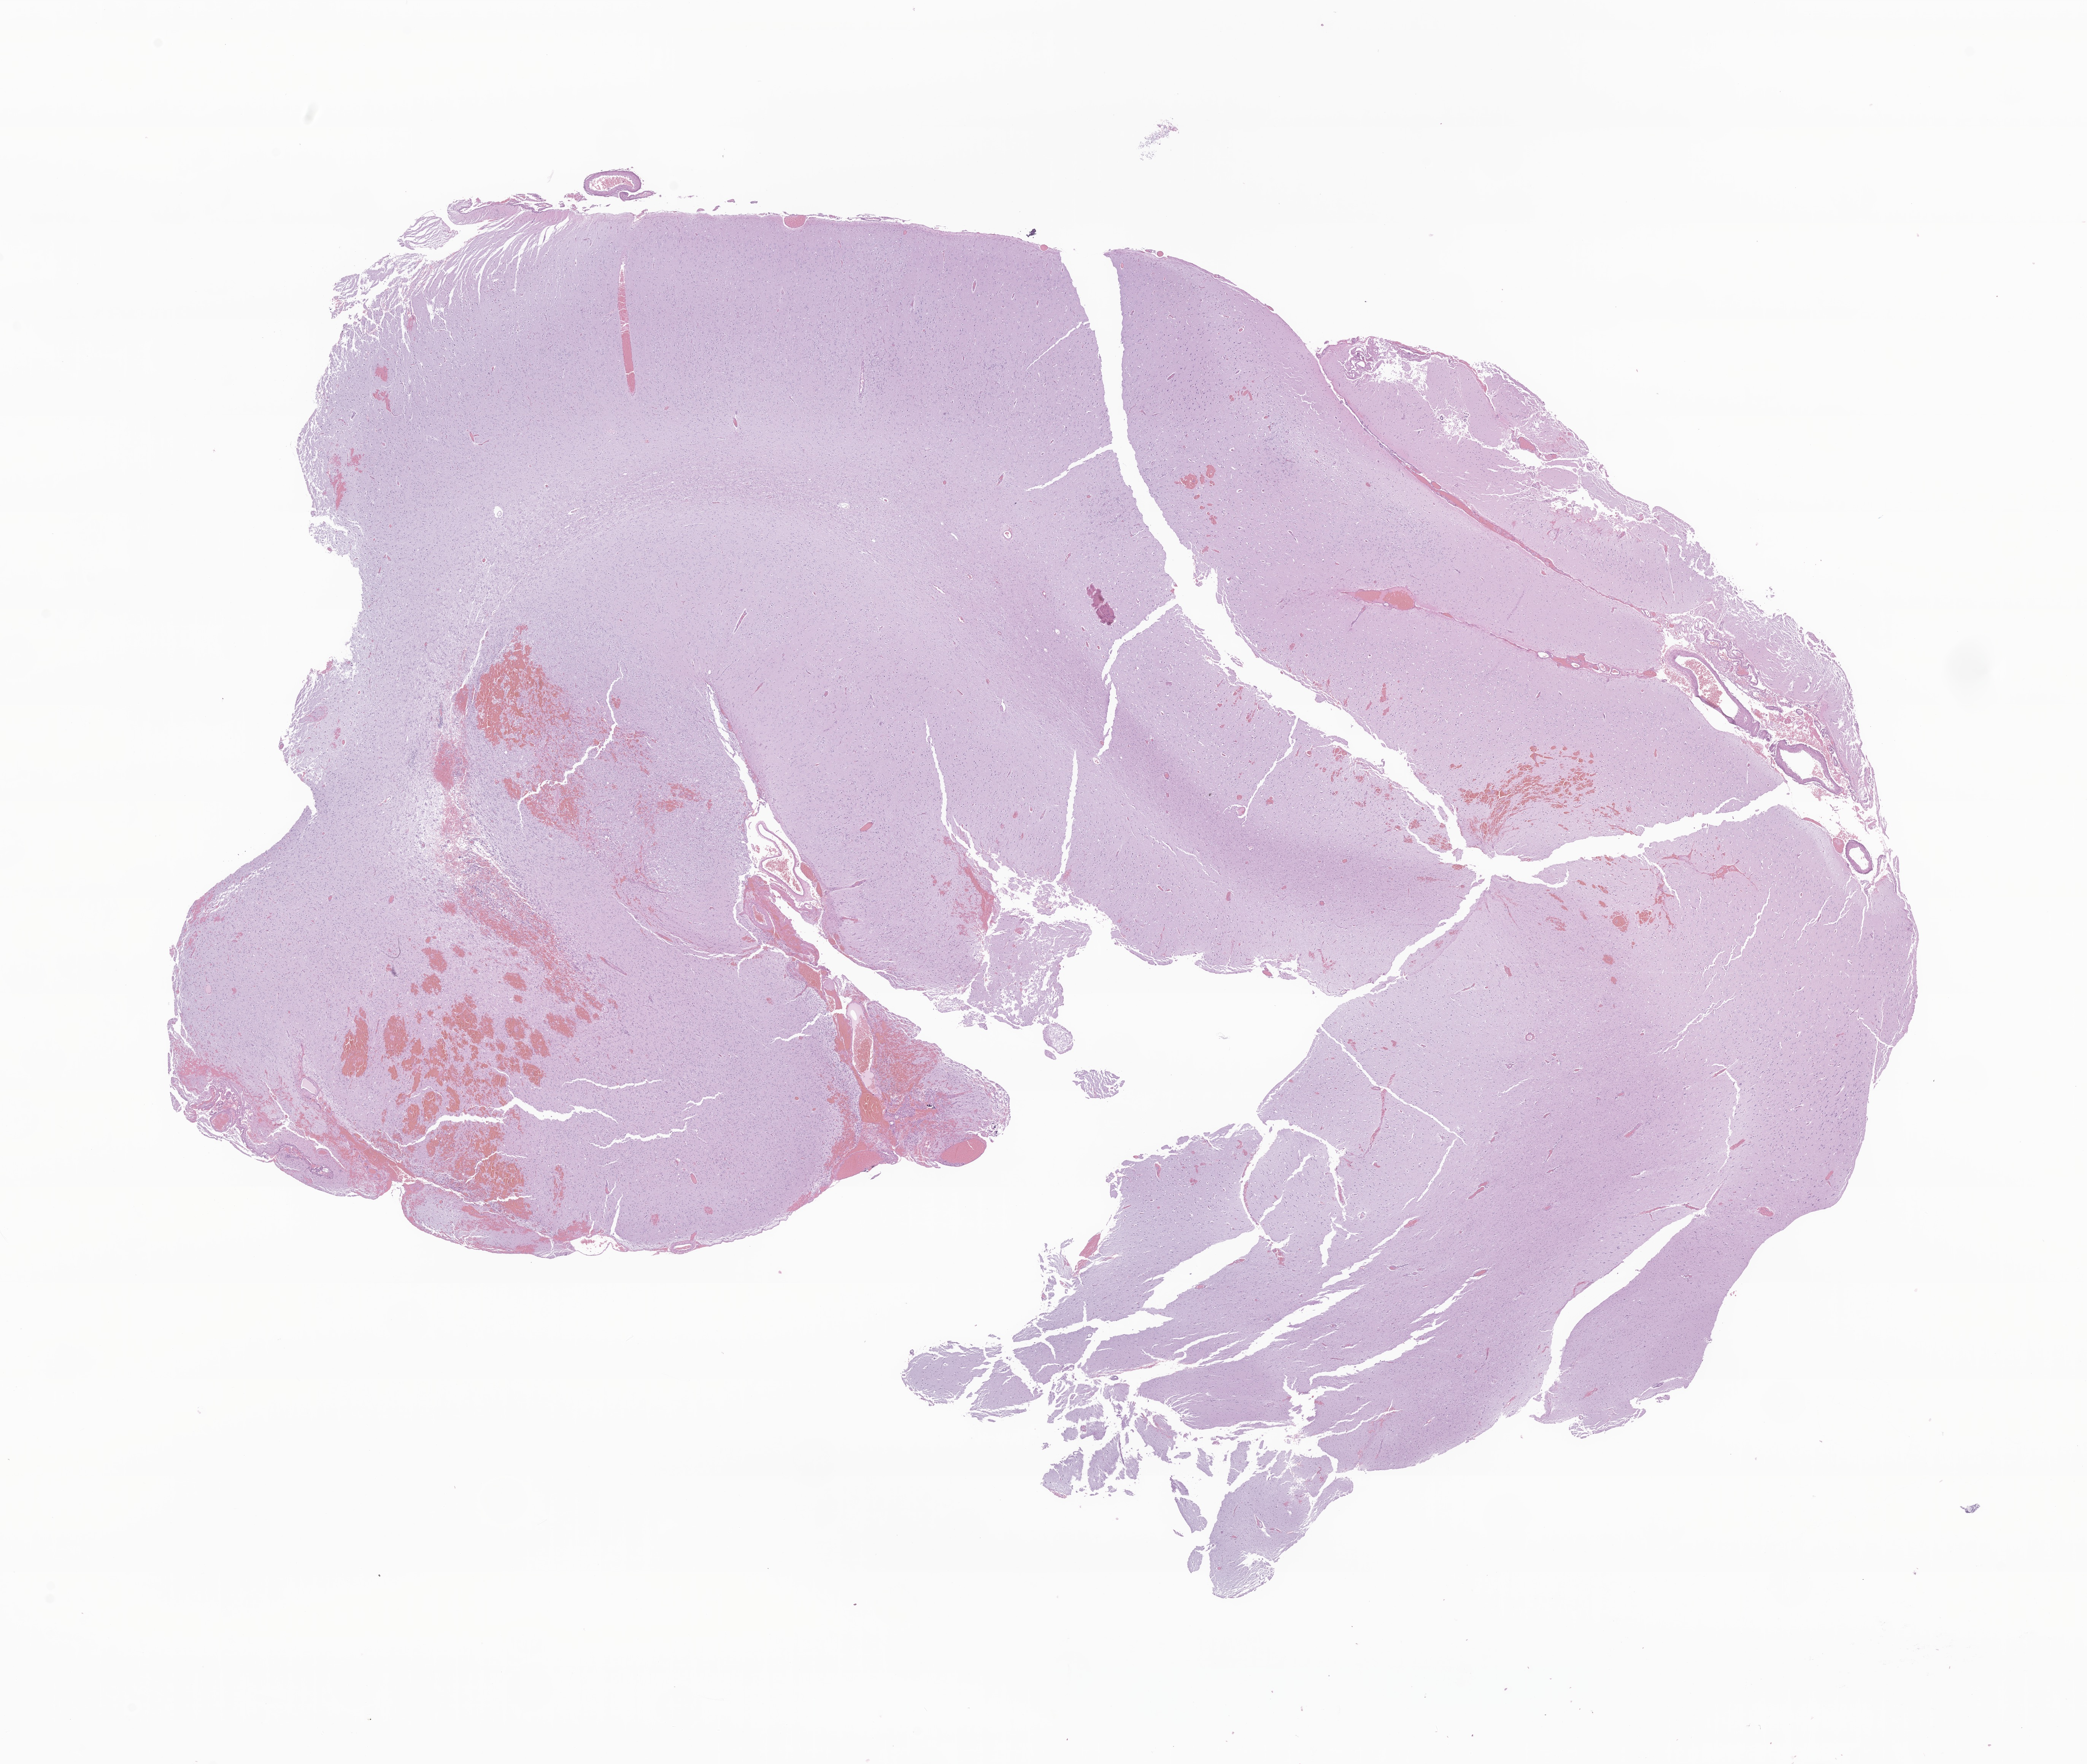
Digitized H&E-stained section of tumor tissue from the temporal lobe — shown as a low-resolution overview of the whole scanned area (about 23.1 x 19.6 mm); formalin-fixed paraffin-embedded section. Patient female; age 172 months (14 years 4 months).
Recorded diagnosis: Glioma, malignant.